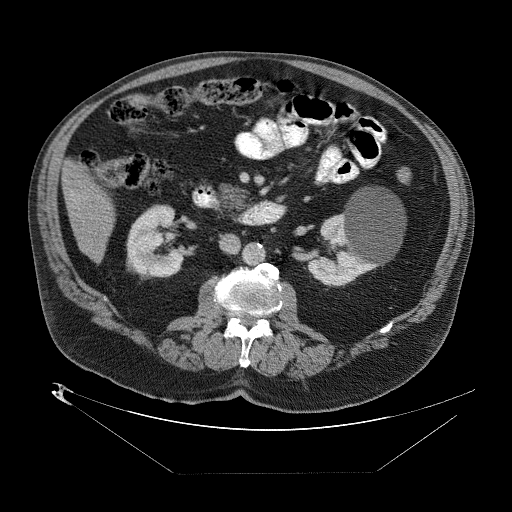
Contrast-enhanced abdominal CT (liver protocol), one axial slice. Position 13 of 89 along the scan axis. Reconstruction kernel STANDARD. 140 kVp. One of 2 acquisitions stored at this slice position. Soft-tissue window (W 400 / L 40 HU). 512 × 512 image matrix, field of view 480 × 480 mm. From the clinical record (not read from this slice): diagnosis: hepatocellular carcinoma (patient treated with transarterial chemoembolisation; whether this scan precedes or follows treatment is not stated here); TNM stage (as recorded): Stage-II; Child-Pugh class: B; tumour differentiation: moderately differentiated; tumour nodularity: multinodular.
Annotated regions visible in this slice (semi-automatically segmented with operator editing):
- abdominal aorta: bounding box [x1, y1, x2, y2] px = [244, 243, 265, 266]
- liver parenchyma outside the tumour (the mass and vessels are separate outlines, so this box may not span the whole liver): [62, 160, 116, 254]
- liver vessels: [68, 190, 88, 245]